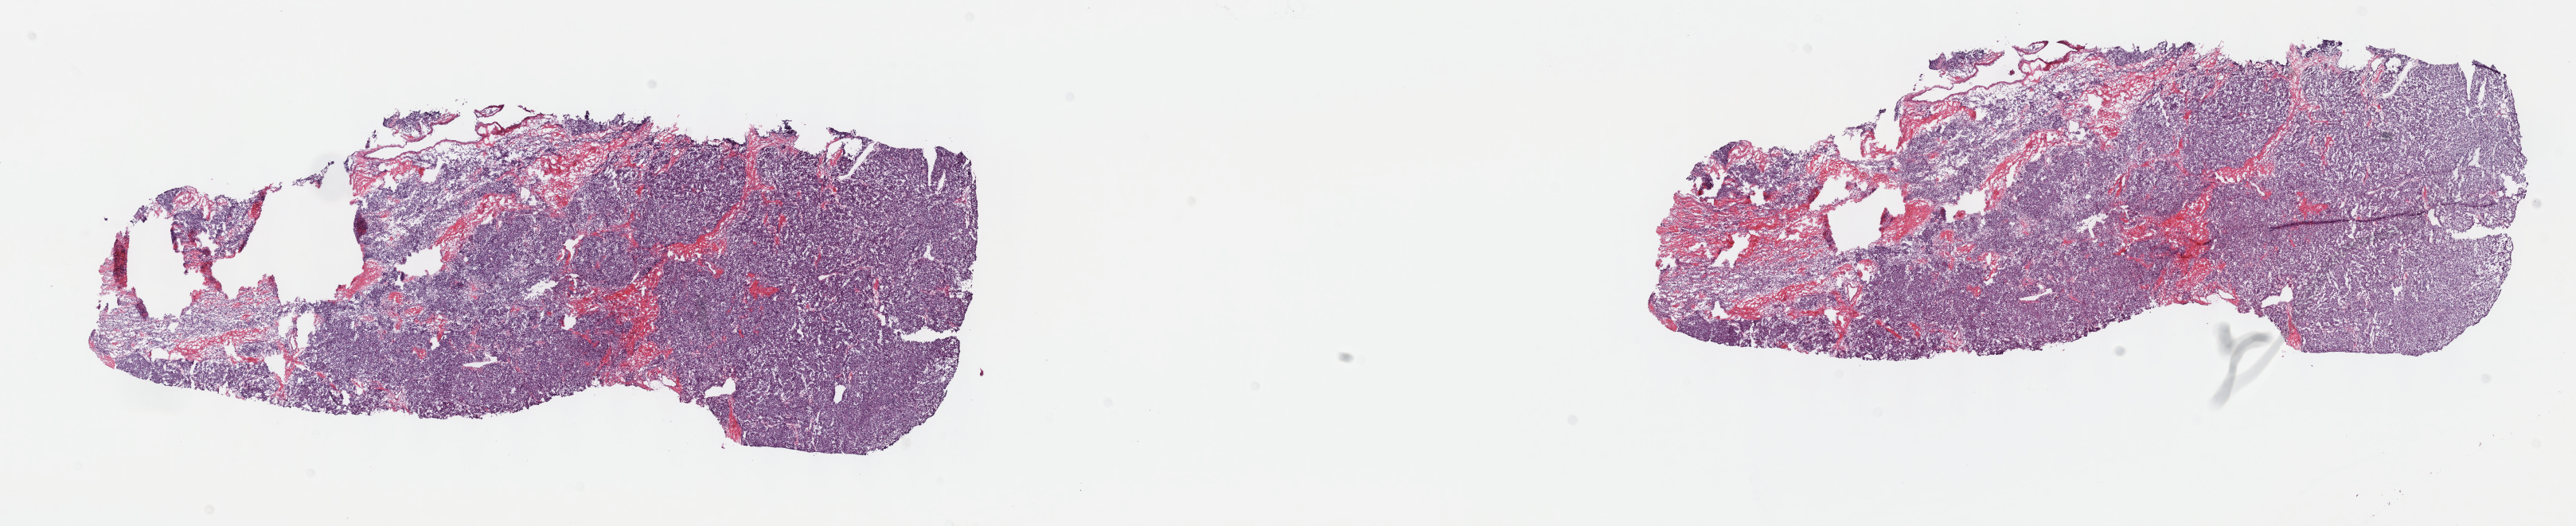
H&E-stained whole-slide image — whole scanned area (about 26.2 x 5.3 mm, from a 40x scan) shown as a low-resolution overview, frozen section from the top of the tissue portion, primary tumour sample from the thymus. Patient: male, age at initial diagnosis 52 years. Composition of this section per pathologist review: tumour cells 100%, tumour nuclei 80%, normal cells 0%, stromal cells 0%, necrosis 0%. Inflammatory infiltration, as recorded: lymphocyte infiltration 2%, monocyte infiltration 0%, neutrophil infiltration 0%.
Diagnosis: Thymoma, type A, malignant.